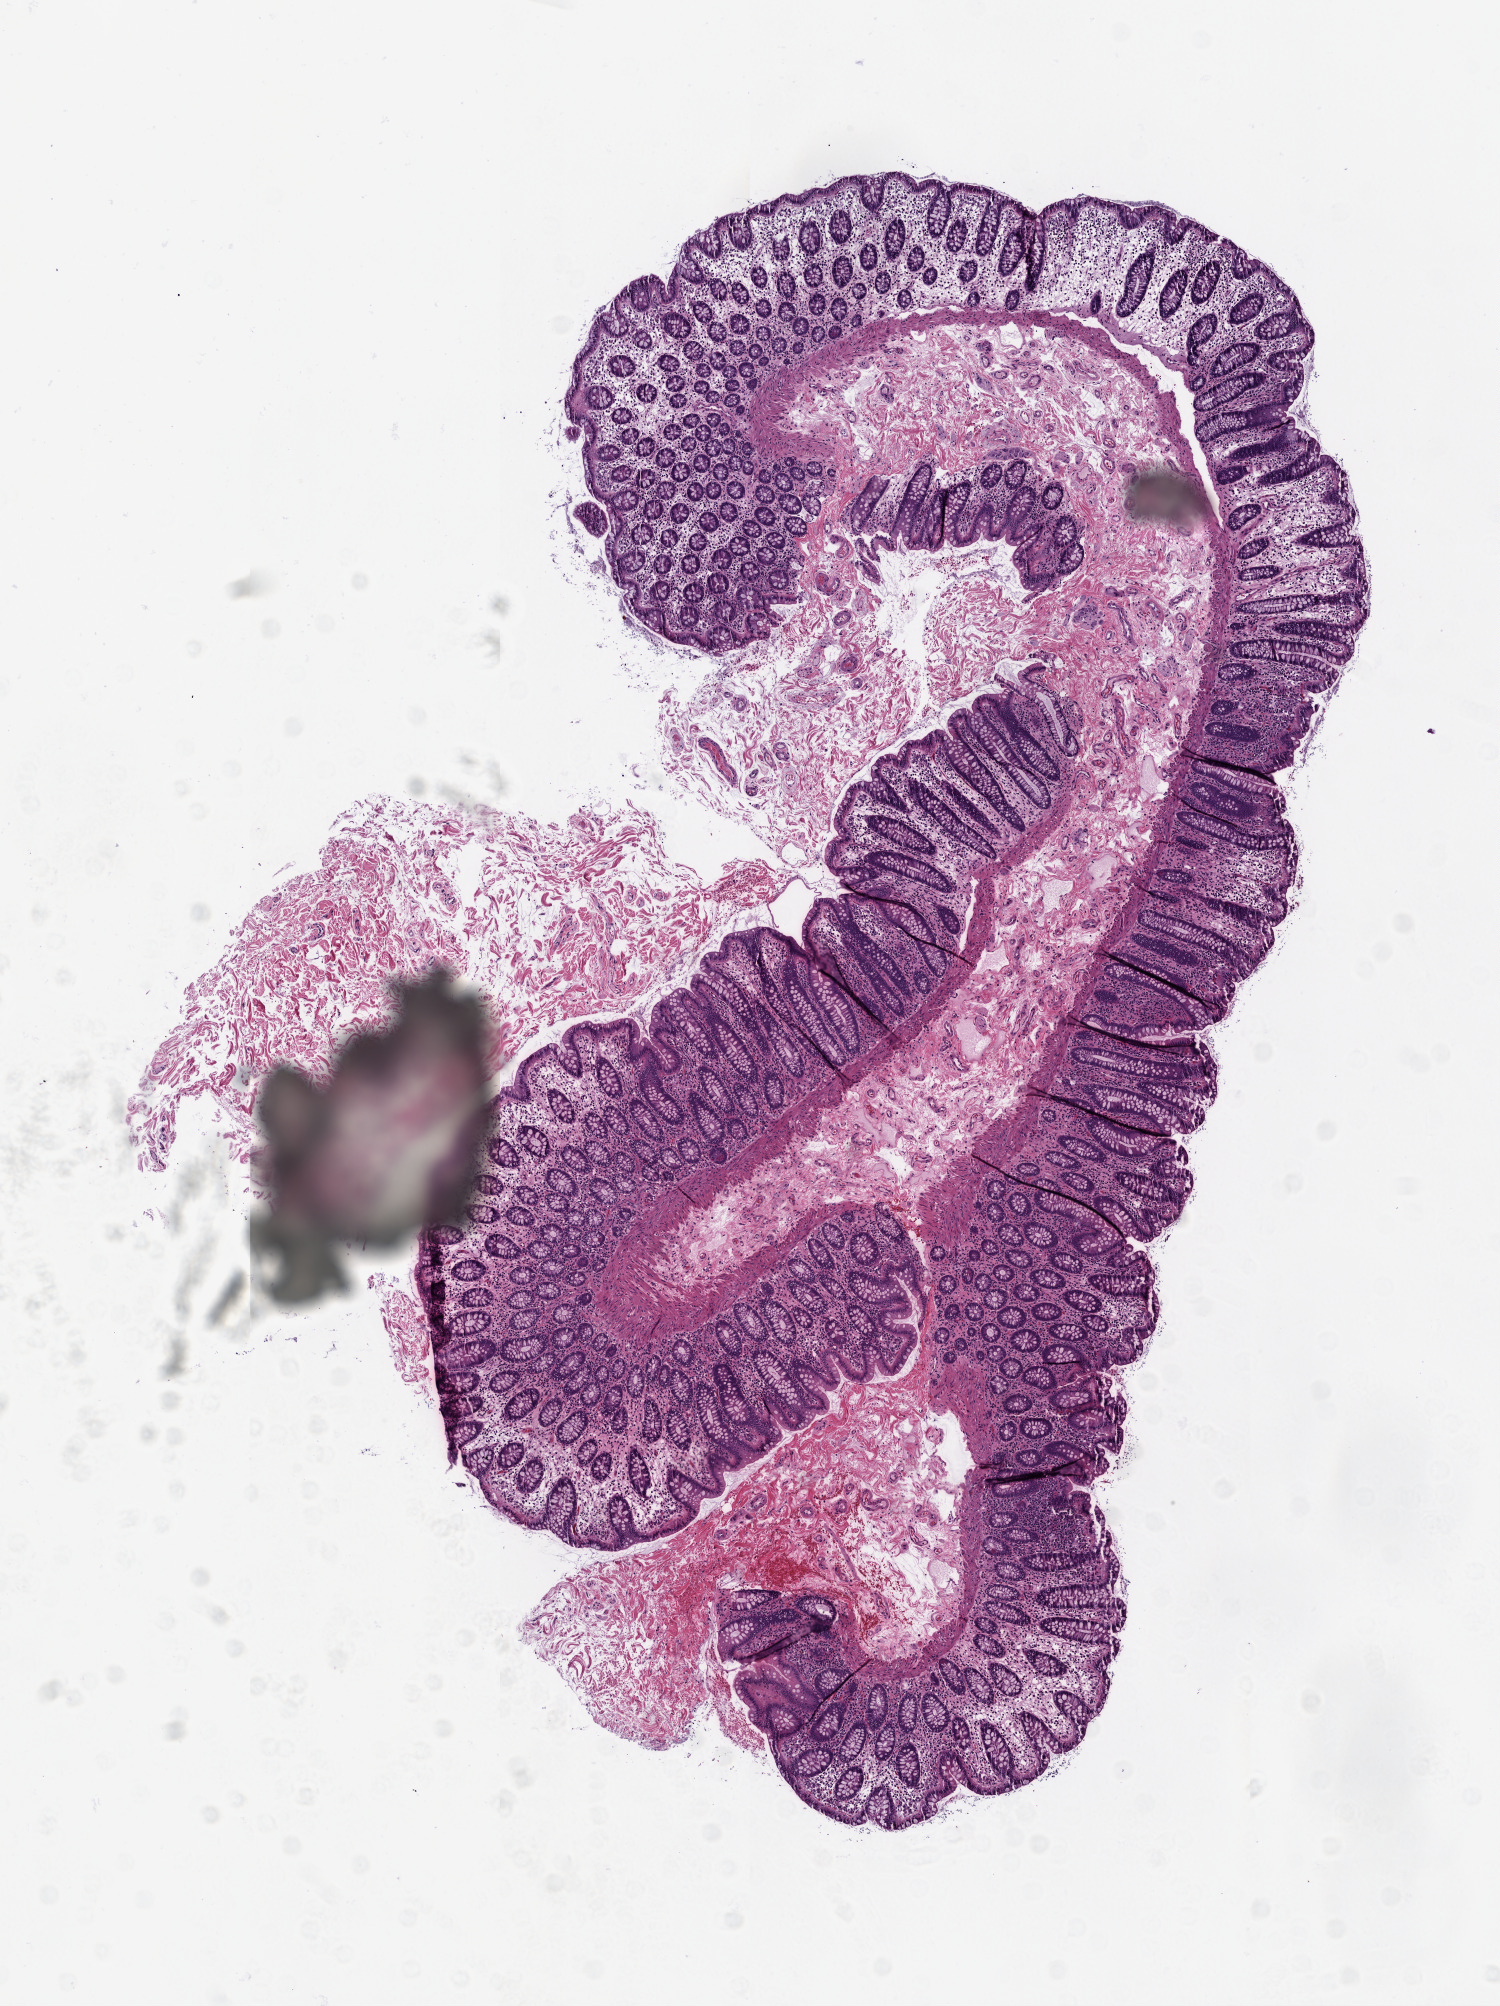
H&E-stained whole-slide image, low-resolution overview of the scanned area, about 6.0 x 8.0 mm (slide scanned at 20x). Frozen section from the top of the tissue portion. Sample: solid tissue normal (non-tumour tissue), colon. Male patient; age at initial diagnosis 73 years.
* this section: solid tissue normal (non-tumour) sample from the same patient
* patient diagnosis: Adenocarcinoma, NOS